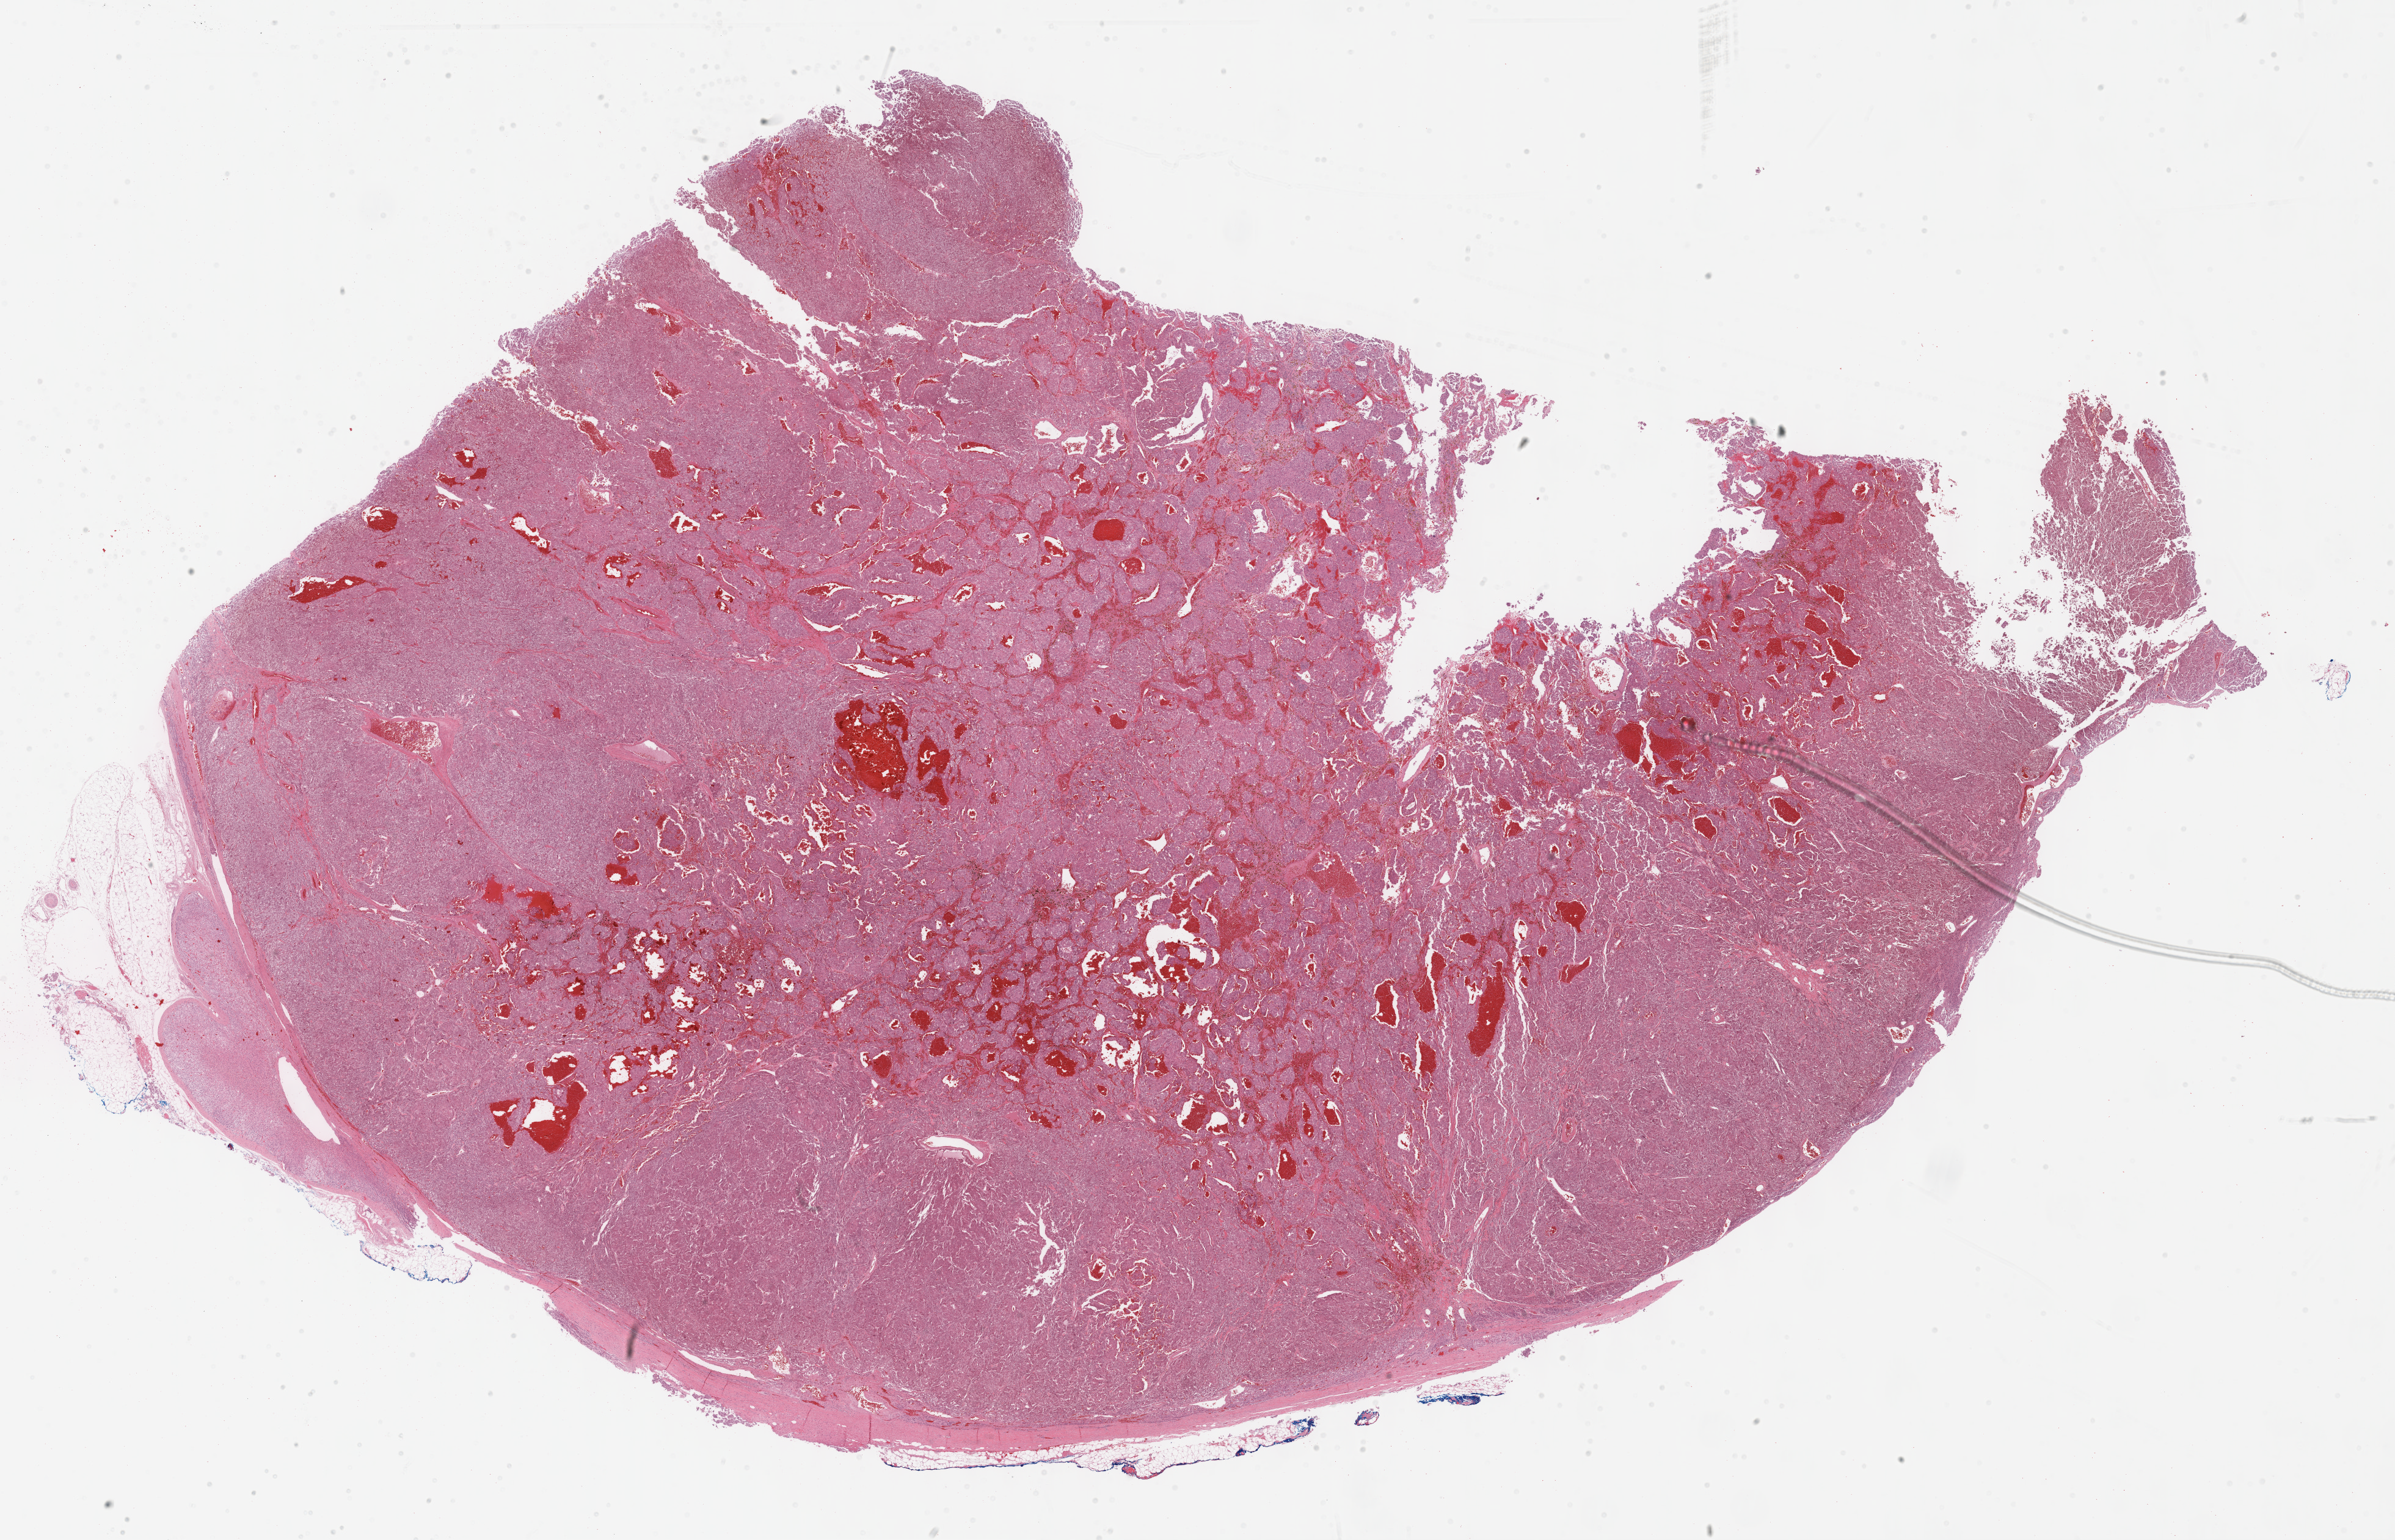
Digitized Hematoxylin and eosin (H&E) stained tissue section (whole slide), whole scanned area (about 31.7 x 20.4 mm) shown as a low-resolution overview. FFPE section. Adrenal gland, primary tumour sample. Female patient; age at initial diagnosis 47 years.
Pathologic diagnosis: Pheochromocytoma, NOS.